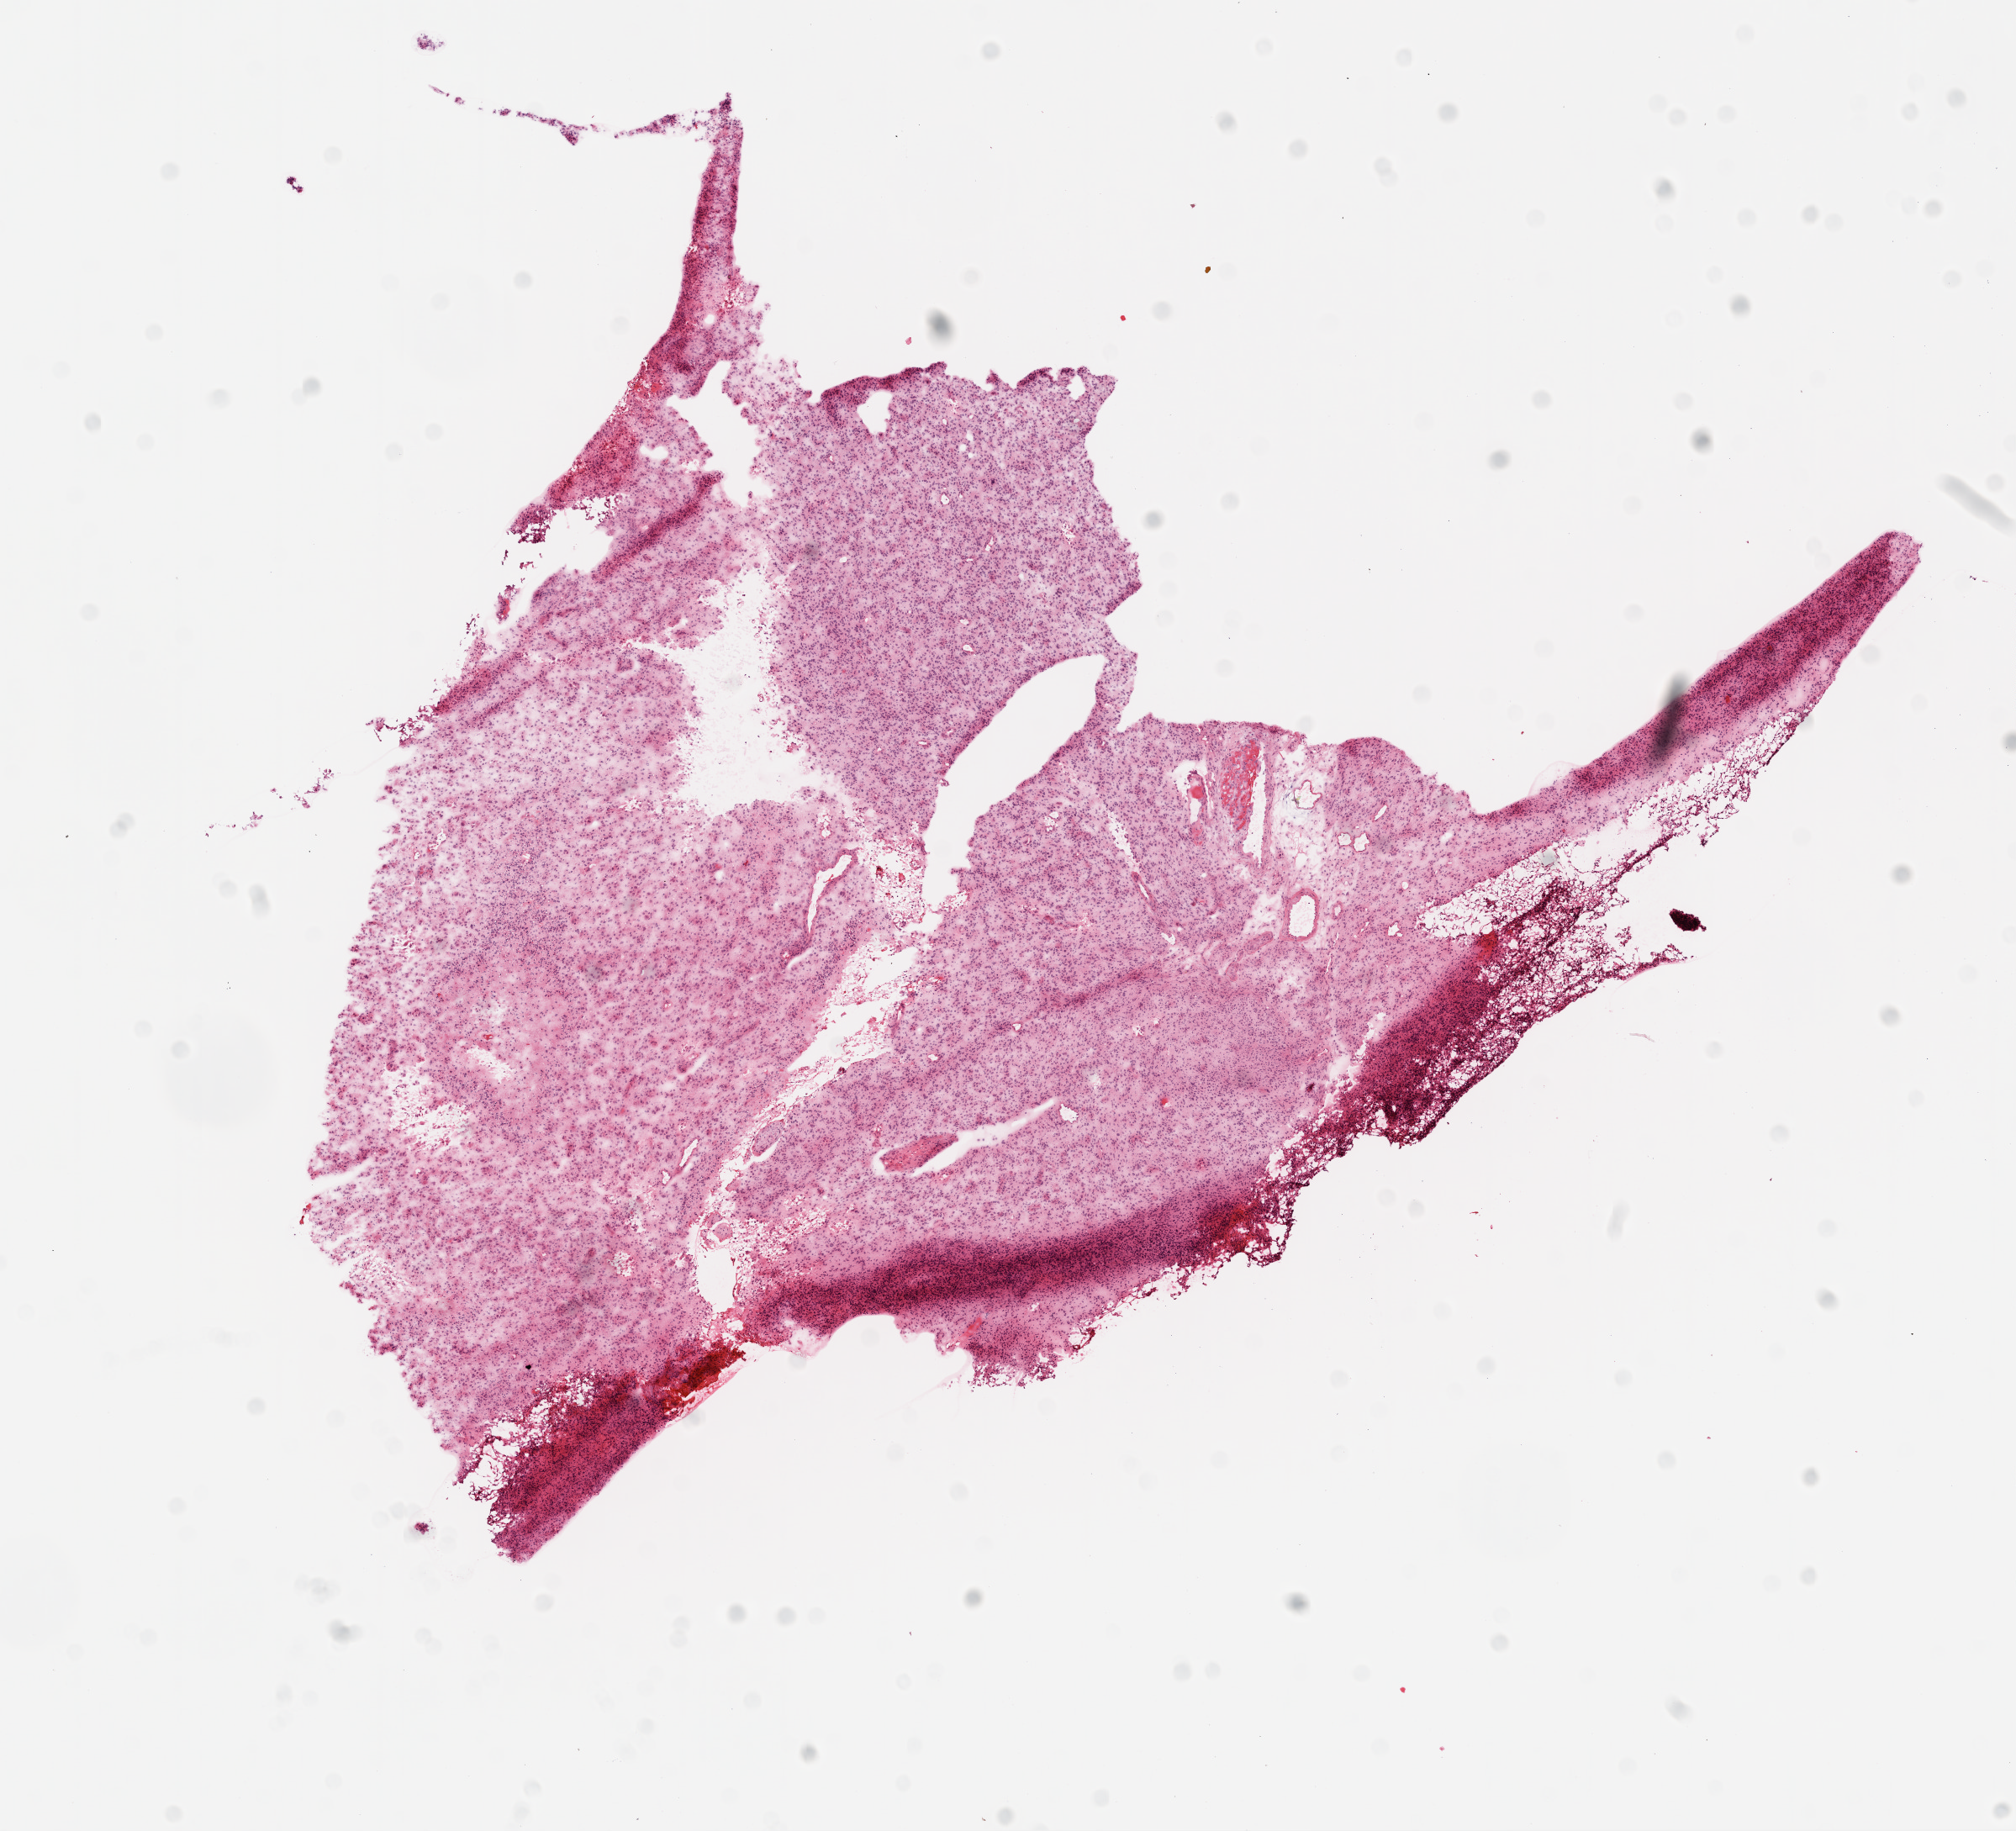
Digitized H&E tissue section (whole slide) — whole scanned area (about 9.7 x 8.8 mm) shown as a low-resolution overview; frozen section from the bottom of the tissue portion; brain, primary tumour sample. Female patient; age at initial diagnosis 30 years. Slide review estimates, as recorded: tumour cells 95%, tumour nuclei 95%, normal cells 0%, stromal cells 0%, necrosis 5%.
Pathologic diagnosis: Glioblastoma.